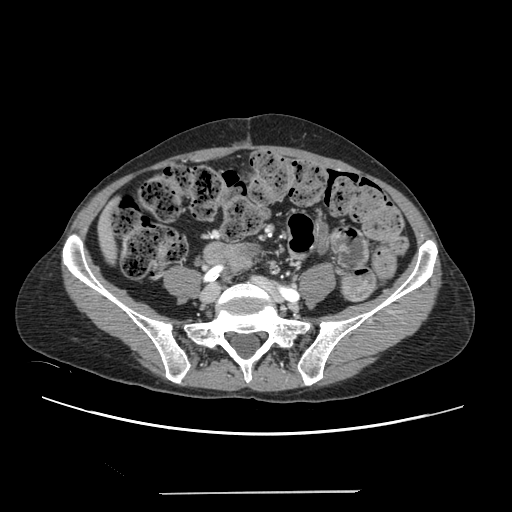
Contrast-enhanced abdominal CT, one axial slice. Slice 11 of 240 in the series (ordered by position). 120 kVp. Soft-tissue window (W 400 / L 40 HU). 1.25 mm slice thickness. 512 × 512 image matrix. Female patient, age 60 years. Case-level facts recorded for this patient, not image findings: diagnosis: colorectal cancer liver metastases, imaged before liver resection; multiple liver metastases: no; largest metastasis: 1.5 cm; disease in both lobes: no.
Annotated regions visible in this slice (manually delineated by an expert):
- liver: bounding box (x1, y1, x2, y2) in pixels: (101, 217, 114, 258)
- planned liver remnant (the part of the liver to remain after resection): (101, 216, 114, 258)